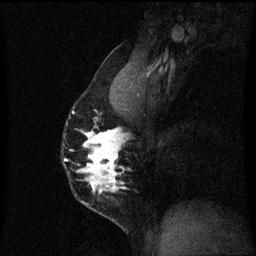
Breast MRI (dynamic contrast-enhanced), one sagittal slice; slice 40 of 60 in the series (ordered by position); dynamic contrast-enhanced series, image 2 of 3 at this slice position (ordered by acquisition); 1.5 T; TE 4.2 ms, TR 8.4 ms; 2 mm slice thickness; 256 × 256 image matrix. Patient: female, 40 years.
Outlined on this slice (semi-automatically segmented with operator editing):
- analysis volume of interest (the breast-tissue region the enhancement analysis was run in; not a lesion): bounding box (x1, y1, x2, y2) in pixels: (63, 96, 126, 211)
- tumour enhancement mask (voxels above the 70 % enhancement threshold inside the analysis volume of interest): (73, 112, 125, 205)